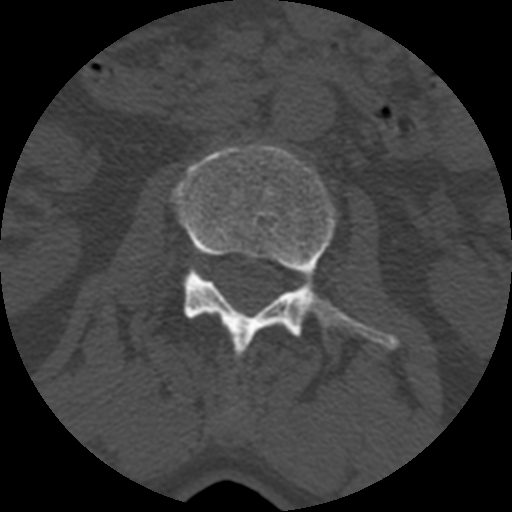
CT including the spine, one axial slice. Slice 333 of 399 in the series (ordered by position). 120 kVp. Bone window (W 1800 / L 400 HU). 1.25 mm slice thickness. 512 × 512 image matrix. Patient age 71 years. From the clinical record (not read from this slice): primary cancer: prostate.
Annotated regions visible in this slice (semi-automatically segmented with operator editing):
- L2 vertebra: bounding box <170,145,398,360> (left, top, right, bottom; pixels)